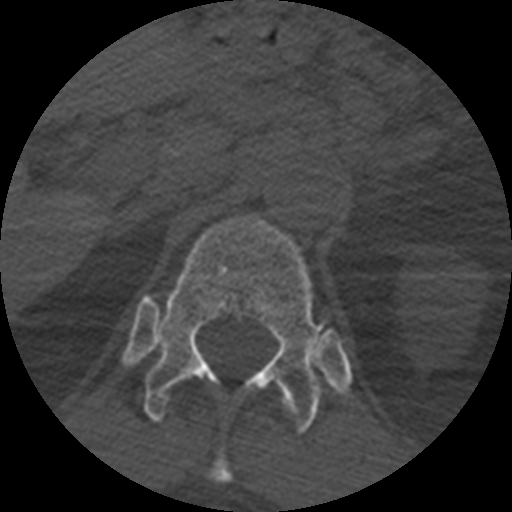
CT including the spine, one axial slice. Slice 390 of 399 in the series (ordered by position). Reconstruction kernel STANDARD. Bone window (W 1800 / L 400 HU). 512 × 512 image matrix. Patient age 71 years. Case-level facts recorded for this patient, not image findings: primary cancer: prostate.
Structures marked on this image (semi-automatically segmented with operator editing):
- T11 vertebra: bounding box (x1, y1, x2, y2) in pixels: (207, 450, 232, 484)
- T12 vertebra: (143, 213, 325, 432)